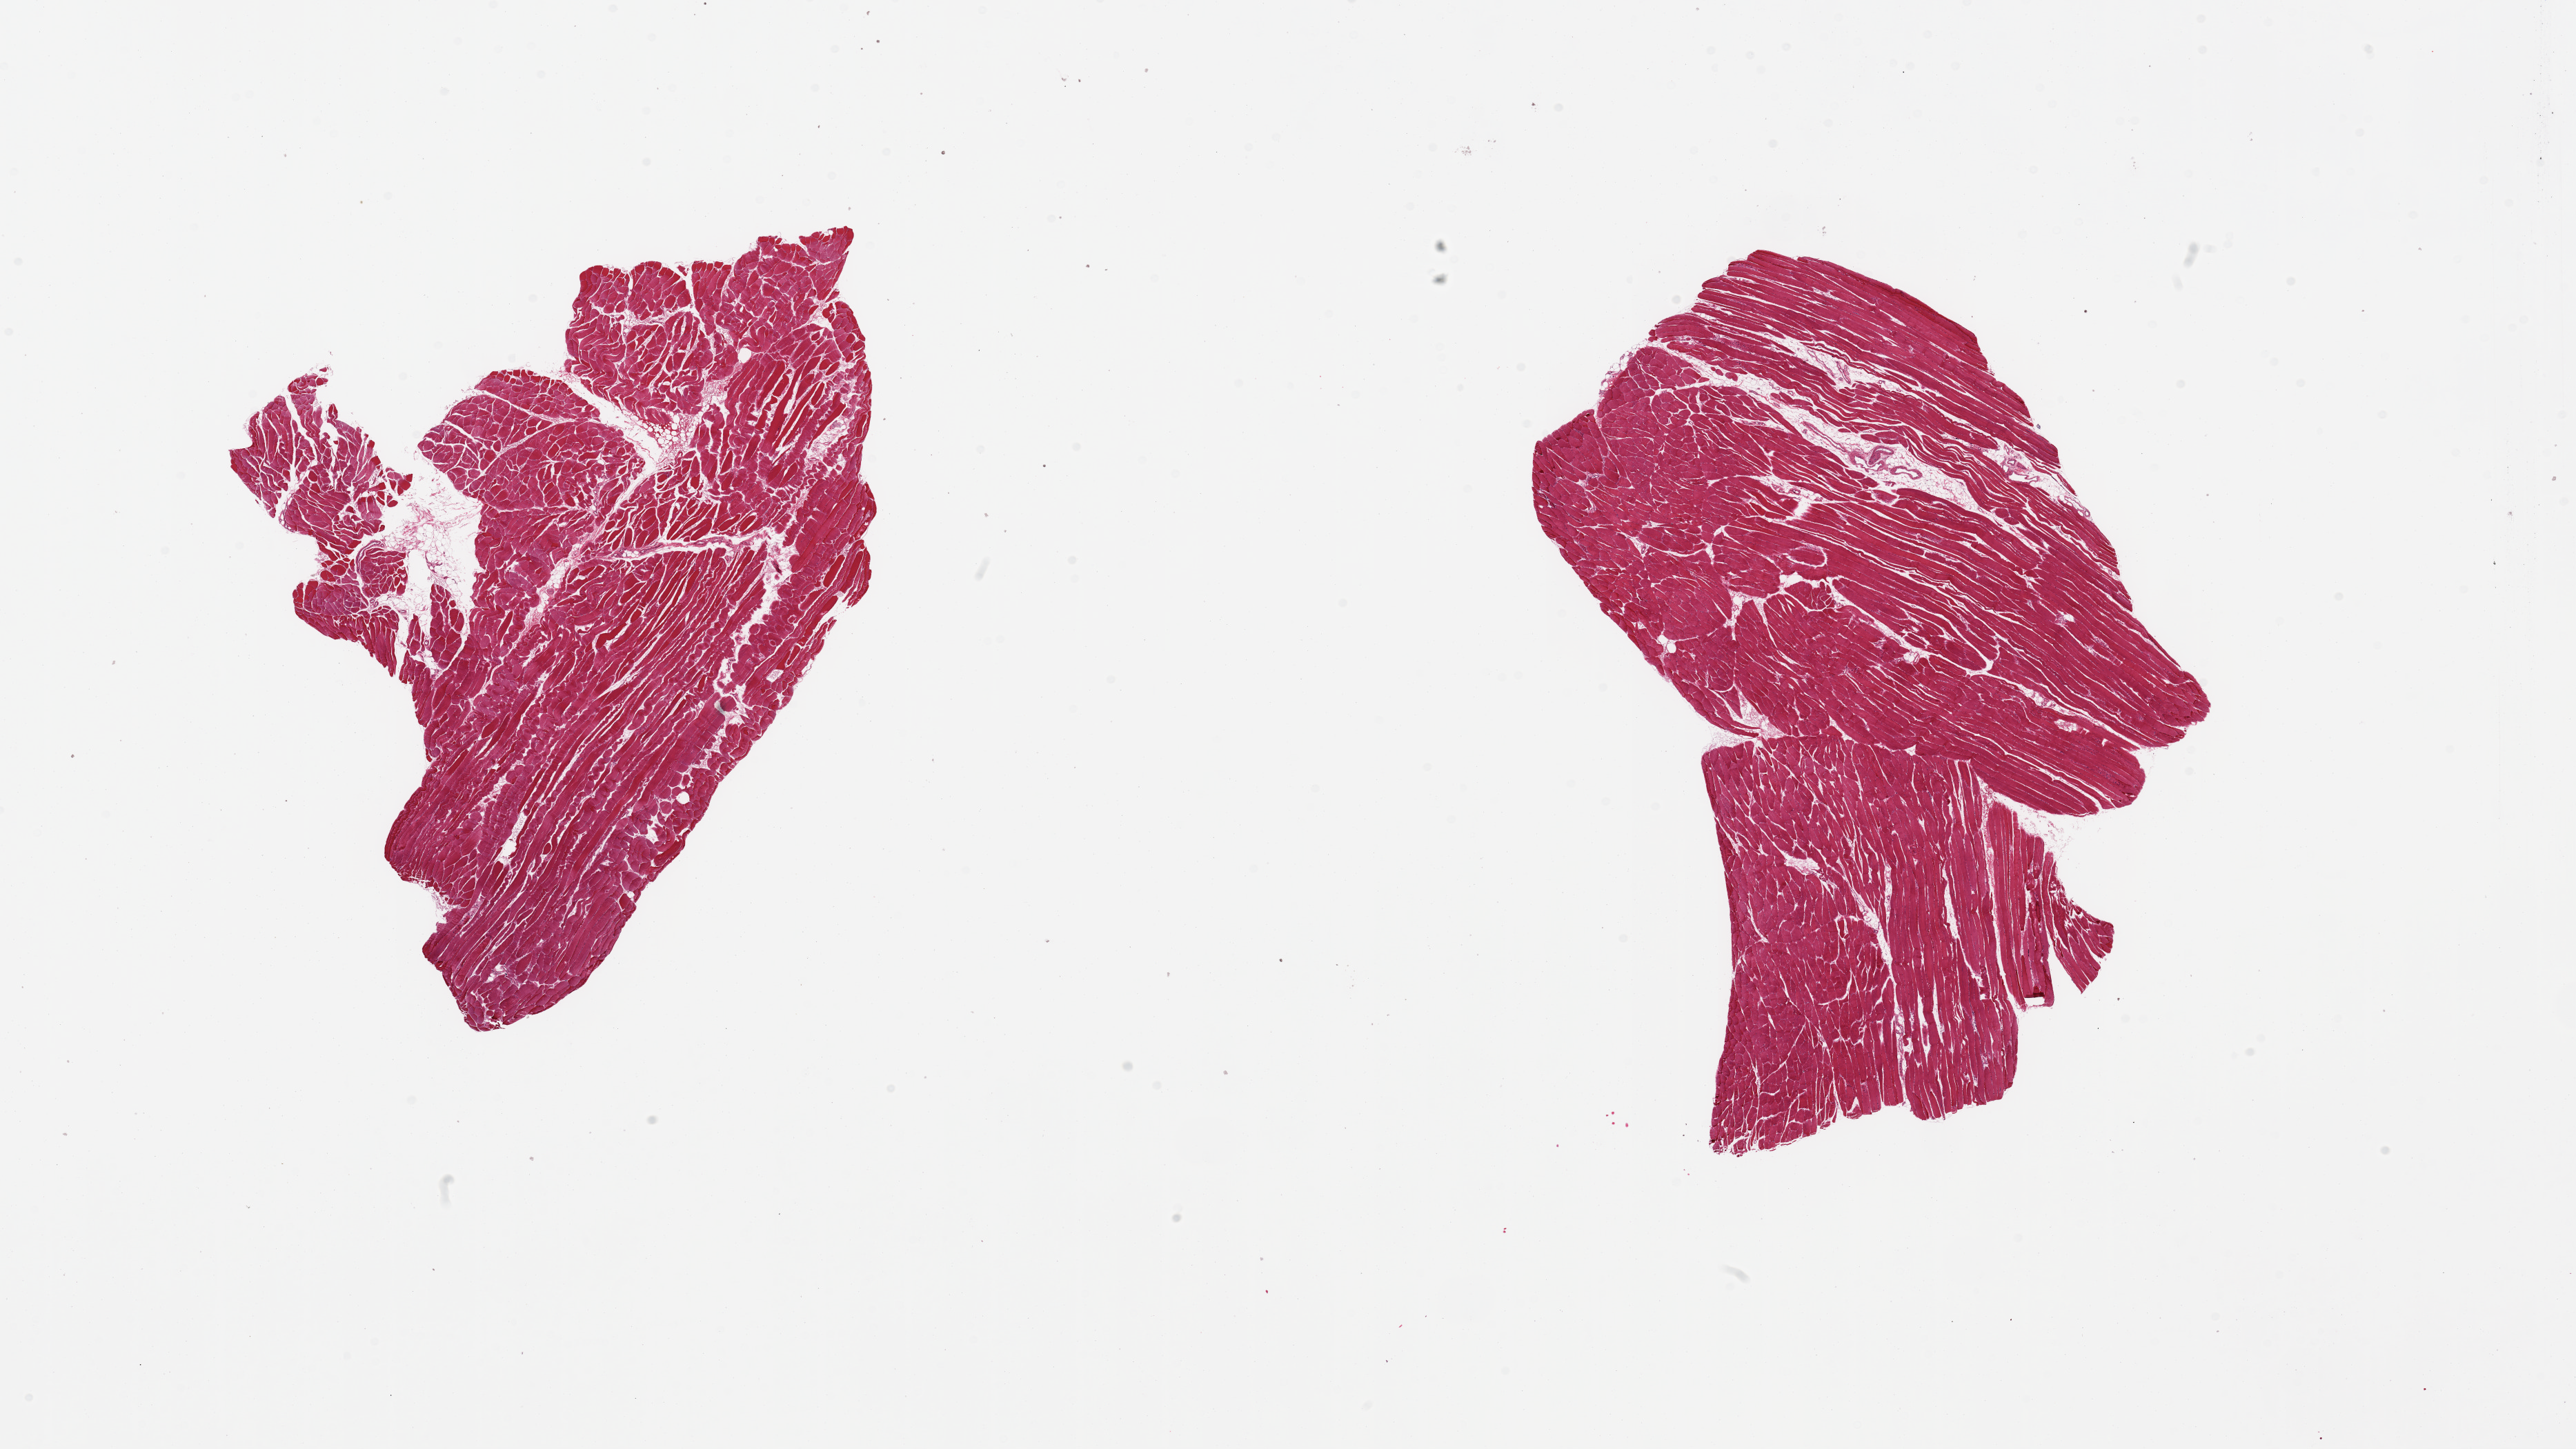
Whole-slide image, H&E stain, brightfield — whole scanned area (about 29.5 x 16.6 mm, from a 20x scan) shown as a low-resolution overview, PAXgene-fixed paraffin-embedded (PFPE) section, section of skeletal muscle (target tissue), donor tissue sample.
- reviewer comment on this tissue sample: 2 pieces, 10-15% interstitial fat